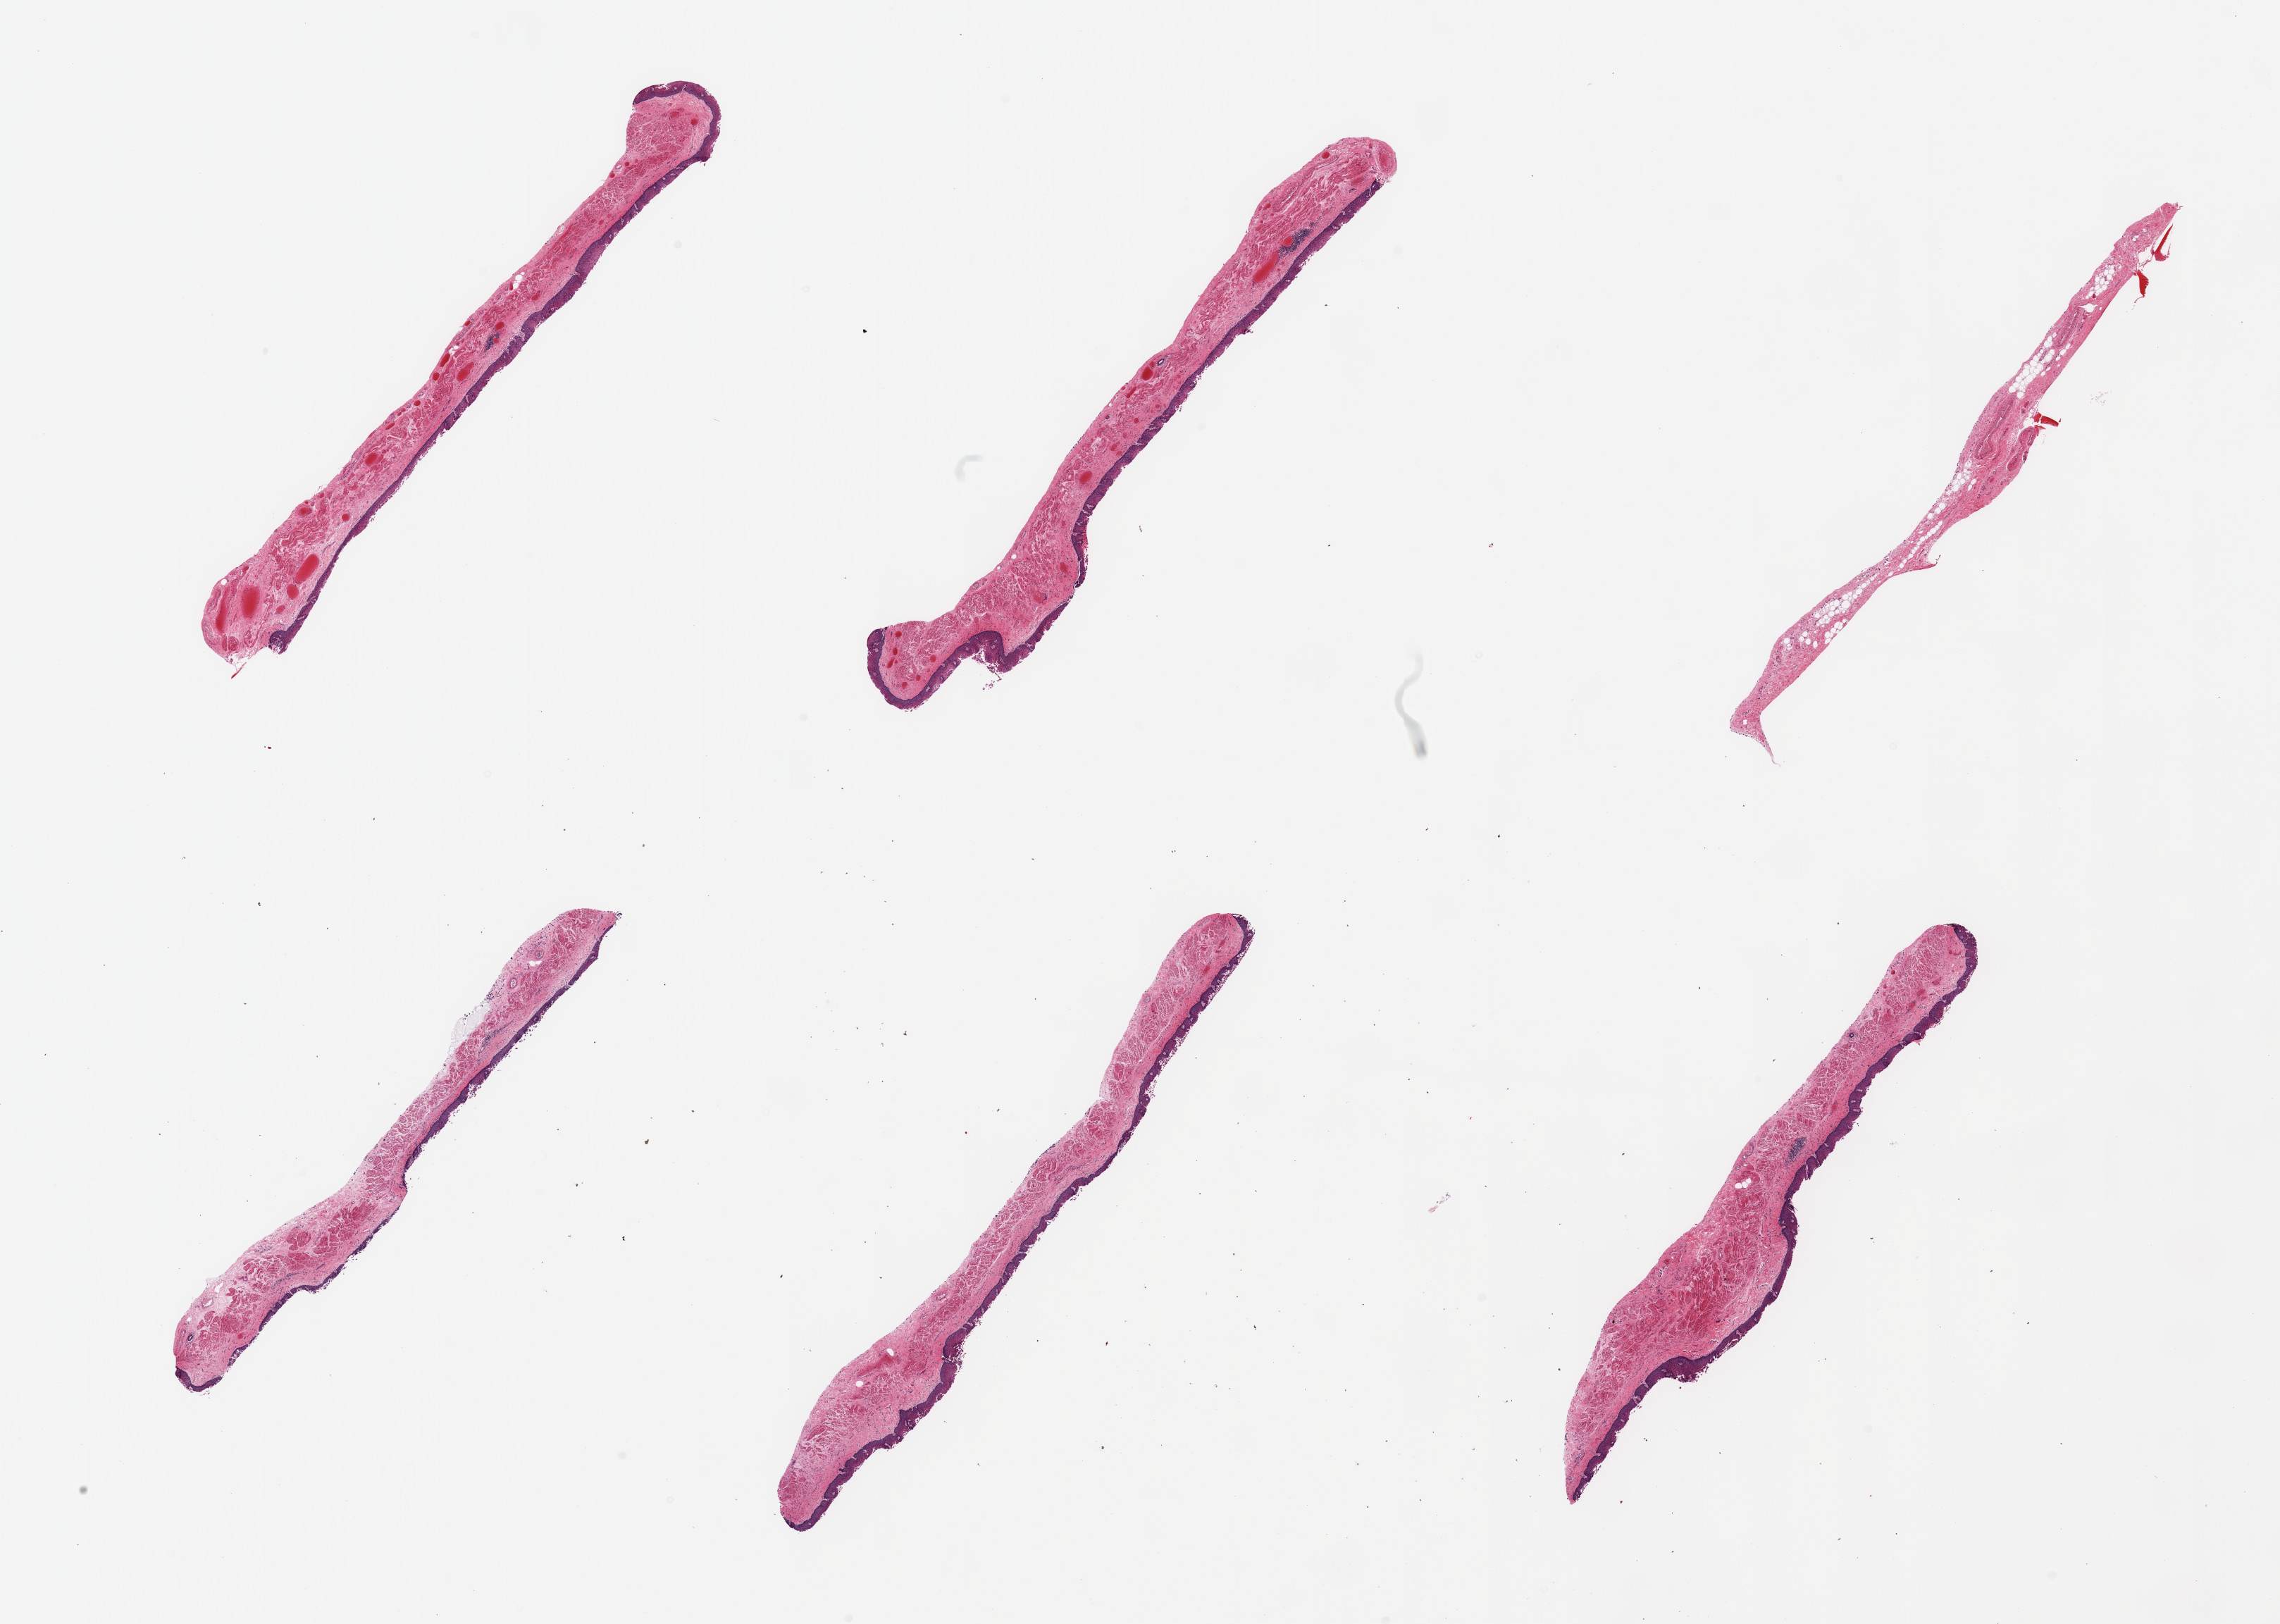
H&E whole-slide image, a low-resolution overview of the entire scanned area, about 25.6 x 18.2 mm (from a 20x scan). PAXgene-fixed paraffin-embedded (PFPE) section. Target tissue: esophageal mucous membrane. Donor tissue sample.
Review note (as recorded): 6 pieces target squamous mucosa up to ~0.15mm, ~20% thickness, early surface sloughing.